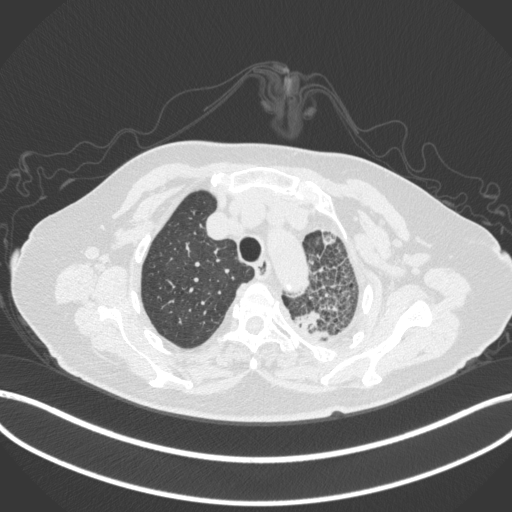
Chest CT, one axial slice. Slice 321 of 399 in the series (ordered by position). Lung window (W 1500 / L -600 HU). 1 mm slice thickness. 512 × 512 image matrix, field of view 400 × 400 mm. Female patient, age 75 years. Case-level facts recorded for this patient, not image findings: clinical TNM (as recorded): T3 N3 M1.
Outlined on this slice (rectangle marked by the reading radiologist):
- lung tumour (recorded histology: adenocarcinoma): bounding box (x1, y1, x2, y2) in pixels: (295, 306, 339, 344)